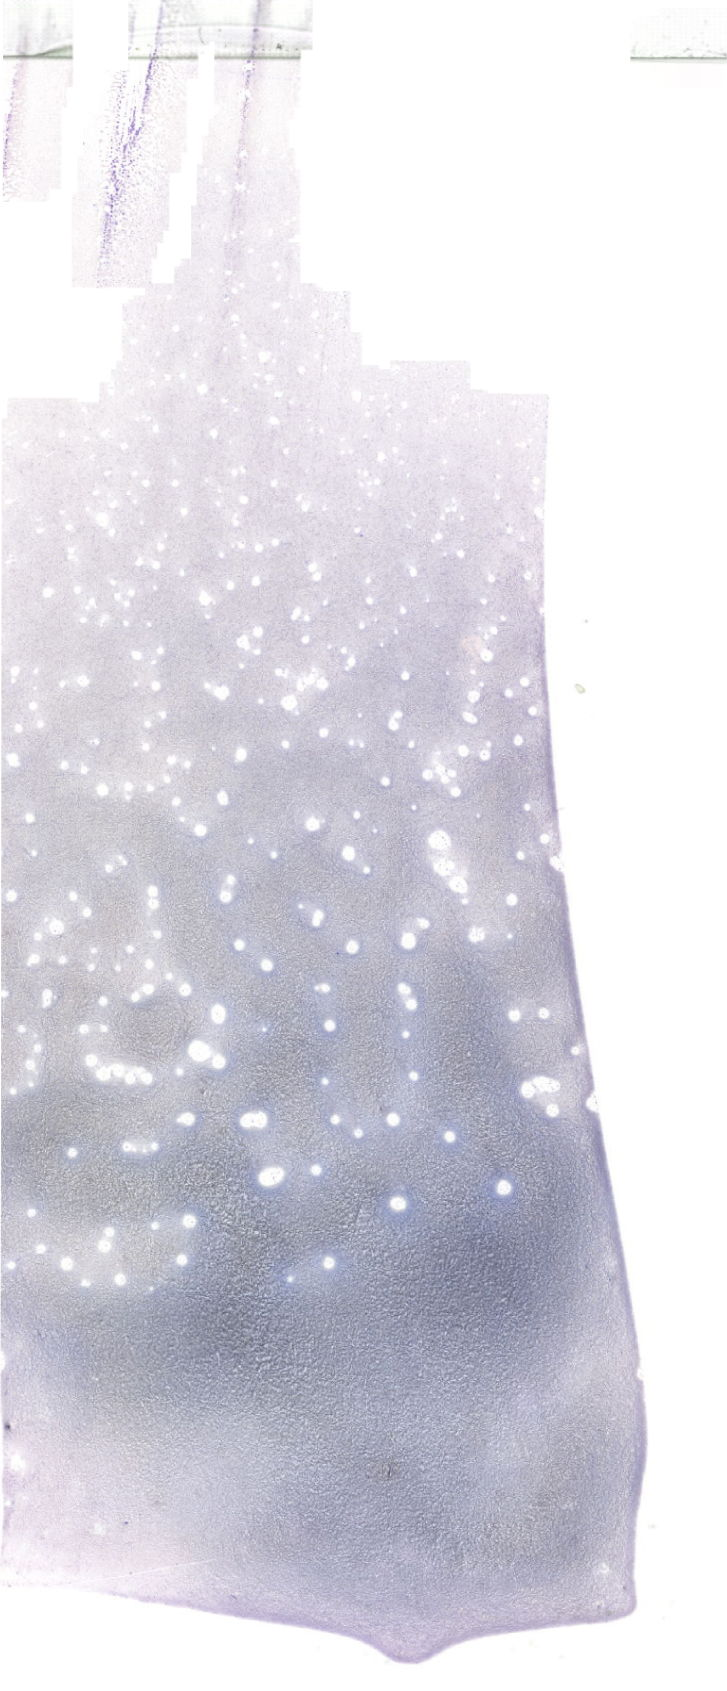
Bone marrow aspirate smear, May-Grünwald-Giemsa (MGG) stain, whole-slide image, shown as a low-resolution overview of the whole scanned area (about 20.6 x 47.9 mm). Male patient.
* diagnosis: Acute Promyelocytic Leukemia with t(15;17)(q24.1;q21.2);PML-RARA